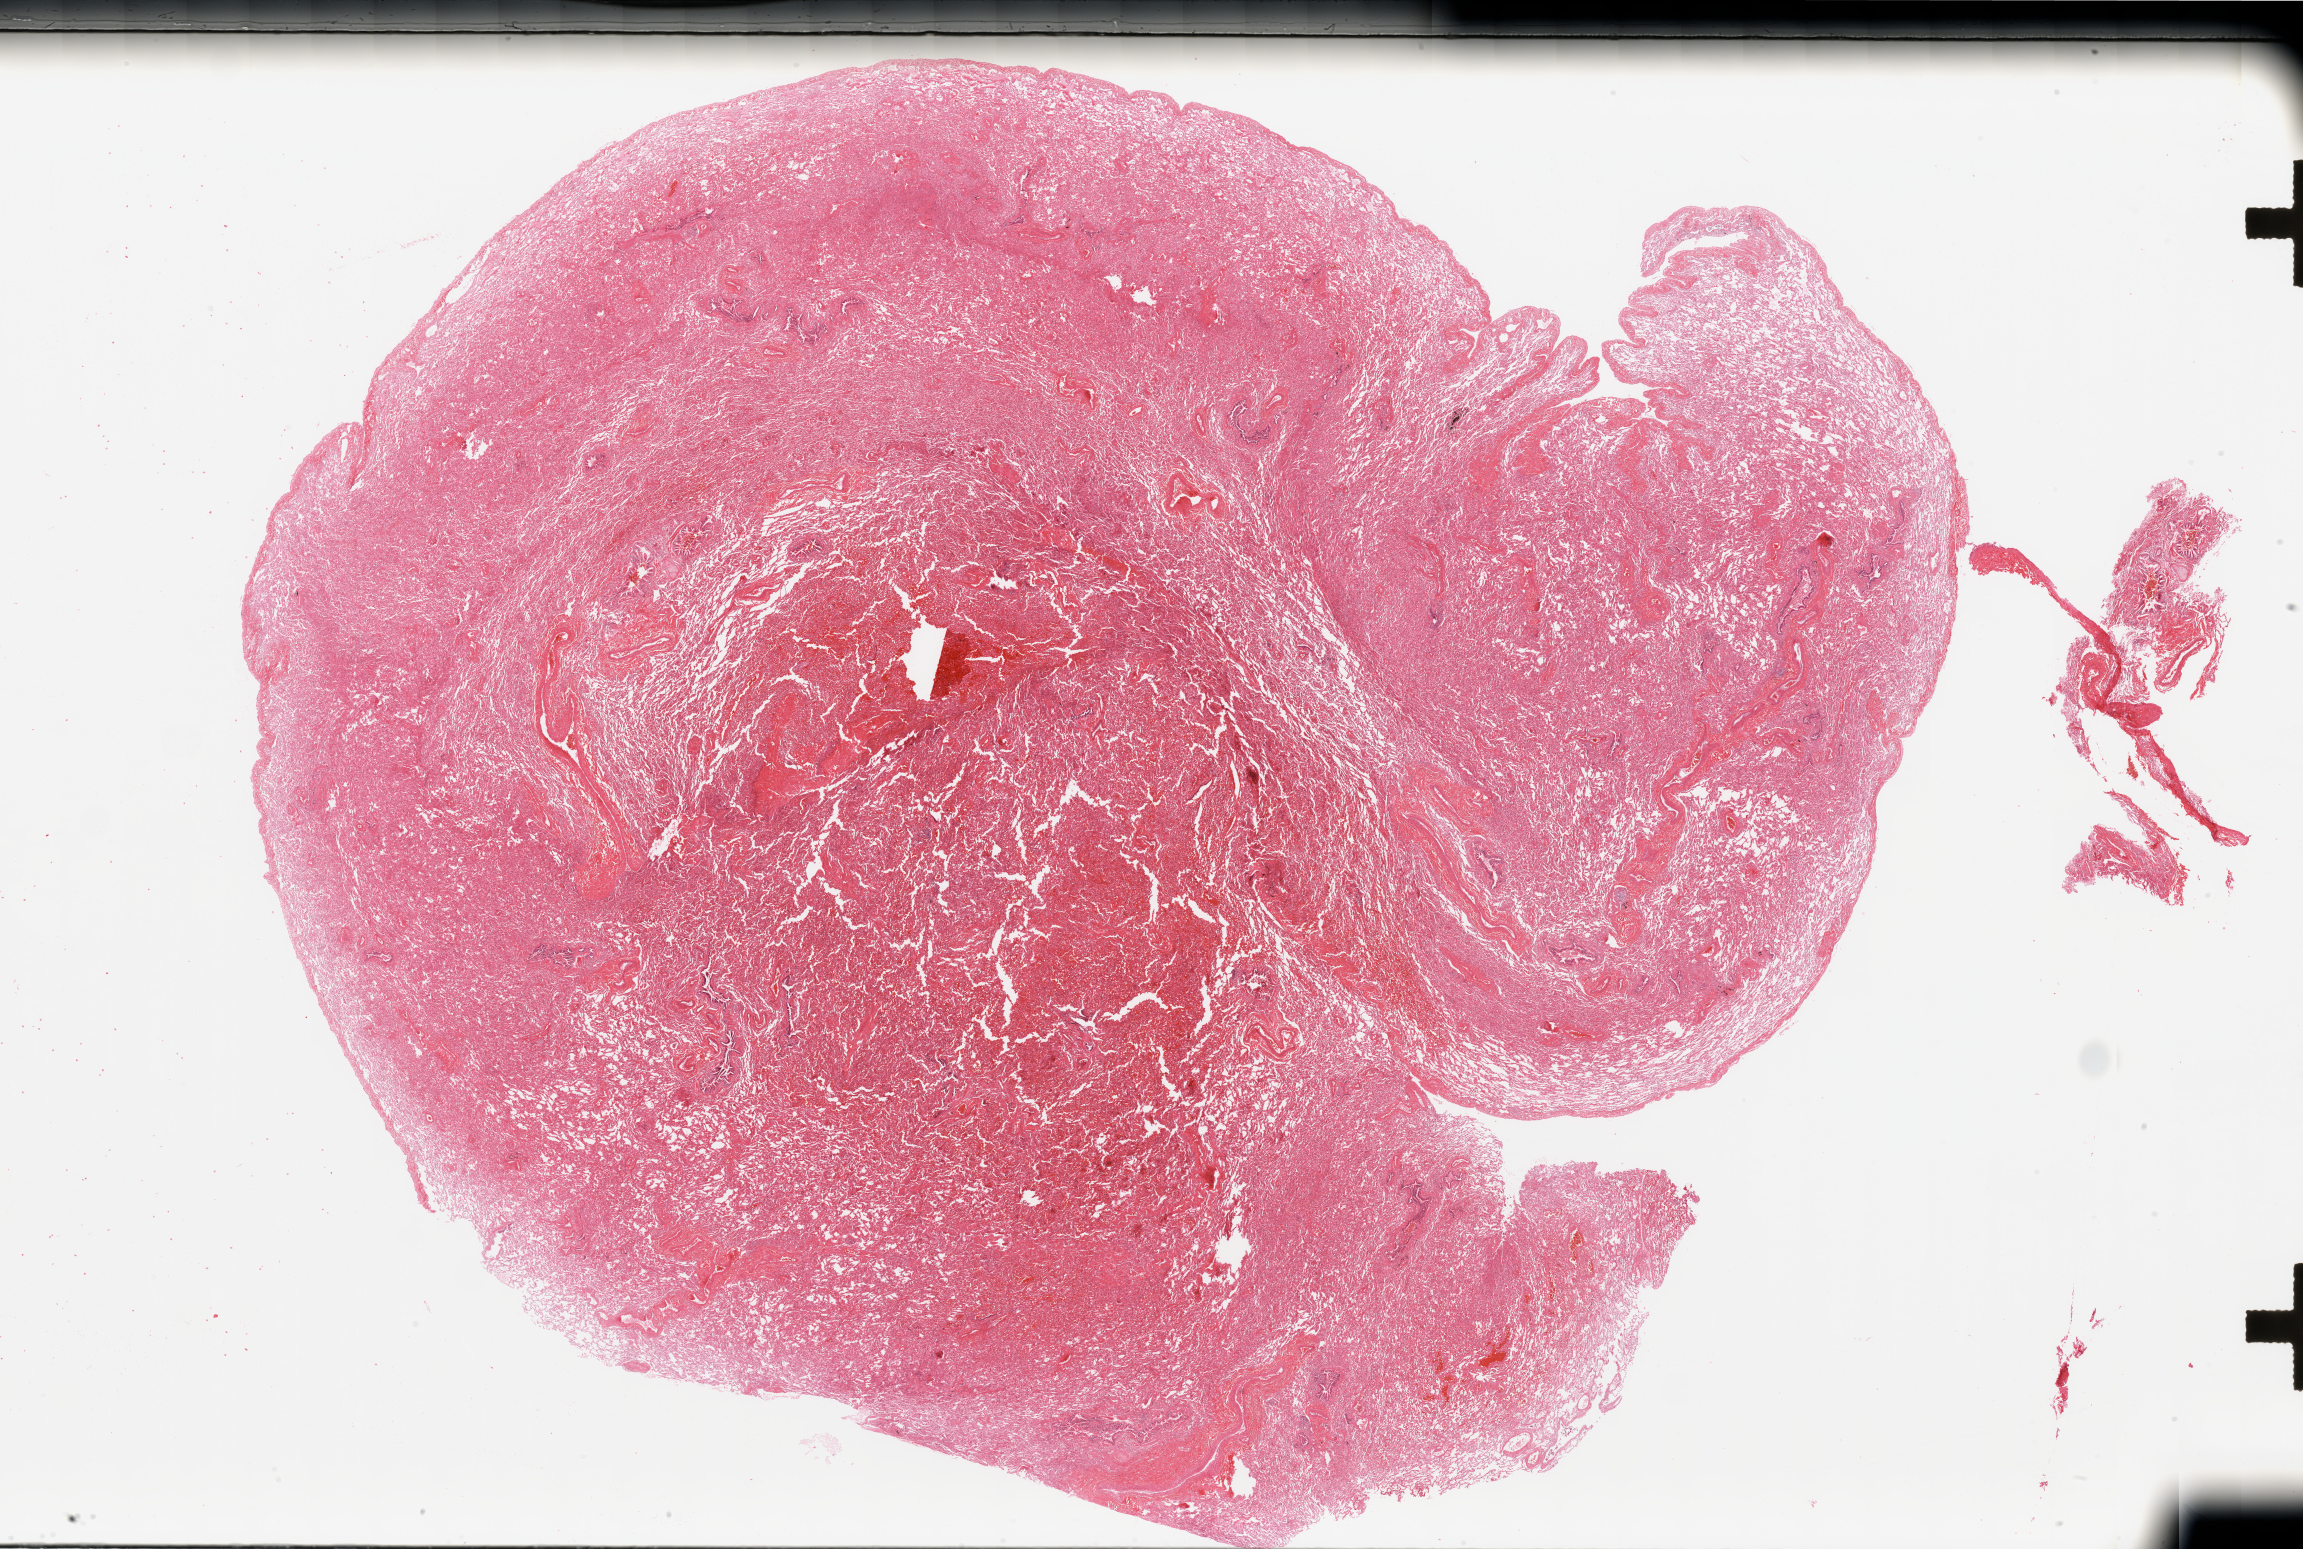
Hematoxylin and eosin (H&E) stained whole-slide image — shown as a low-resolution overview of the whole scanned area (about 36.4 x 24.5 mm, slide scanned at 20x), normal (non-tumour) tissue sample, sampled site: lung. Female, 25 y/o.
• this section: normal (non-tumour) tissue from the same patient
• patient diagnosis: Adenocarcinoma, NOS